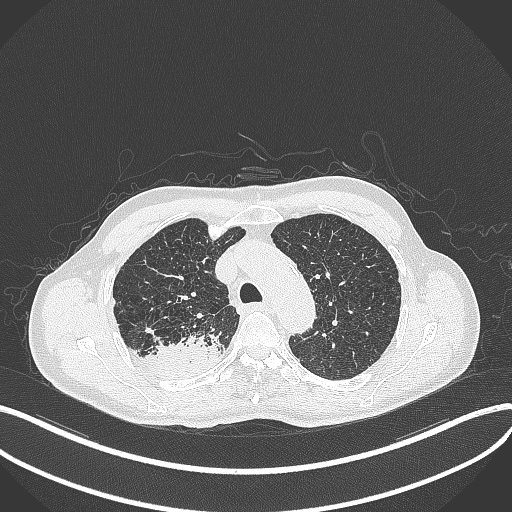
Chest CT, one axial slice. Slice 334 of 428 in the series (ordered by position). Lung window (W 1500 / L -600 HU). 1 mm slice thickness. 512 × 512 image matrix, field of view 400 × 400 mm. Patient: male, 79 years. Case-level facts recorded for this patient, not image findings: clinical TNM (as recorded): T3 N0 M0.
Structures marked on this image (rectangle marked by the reading radiologist):
- lung tumour (recorded histology: adenocarcinoma): bounding box <139,332,225,379> (left, top, right, bottom; pixels)